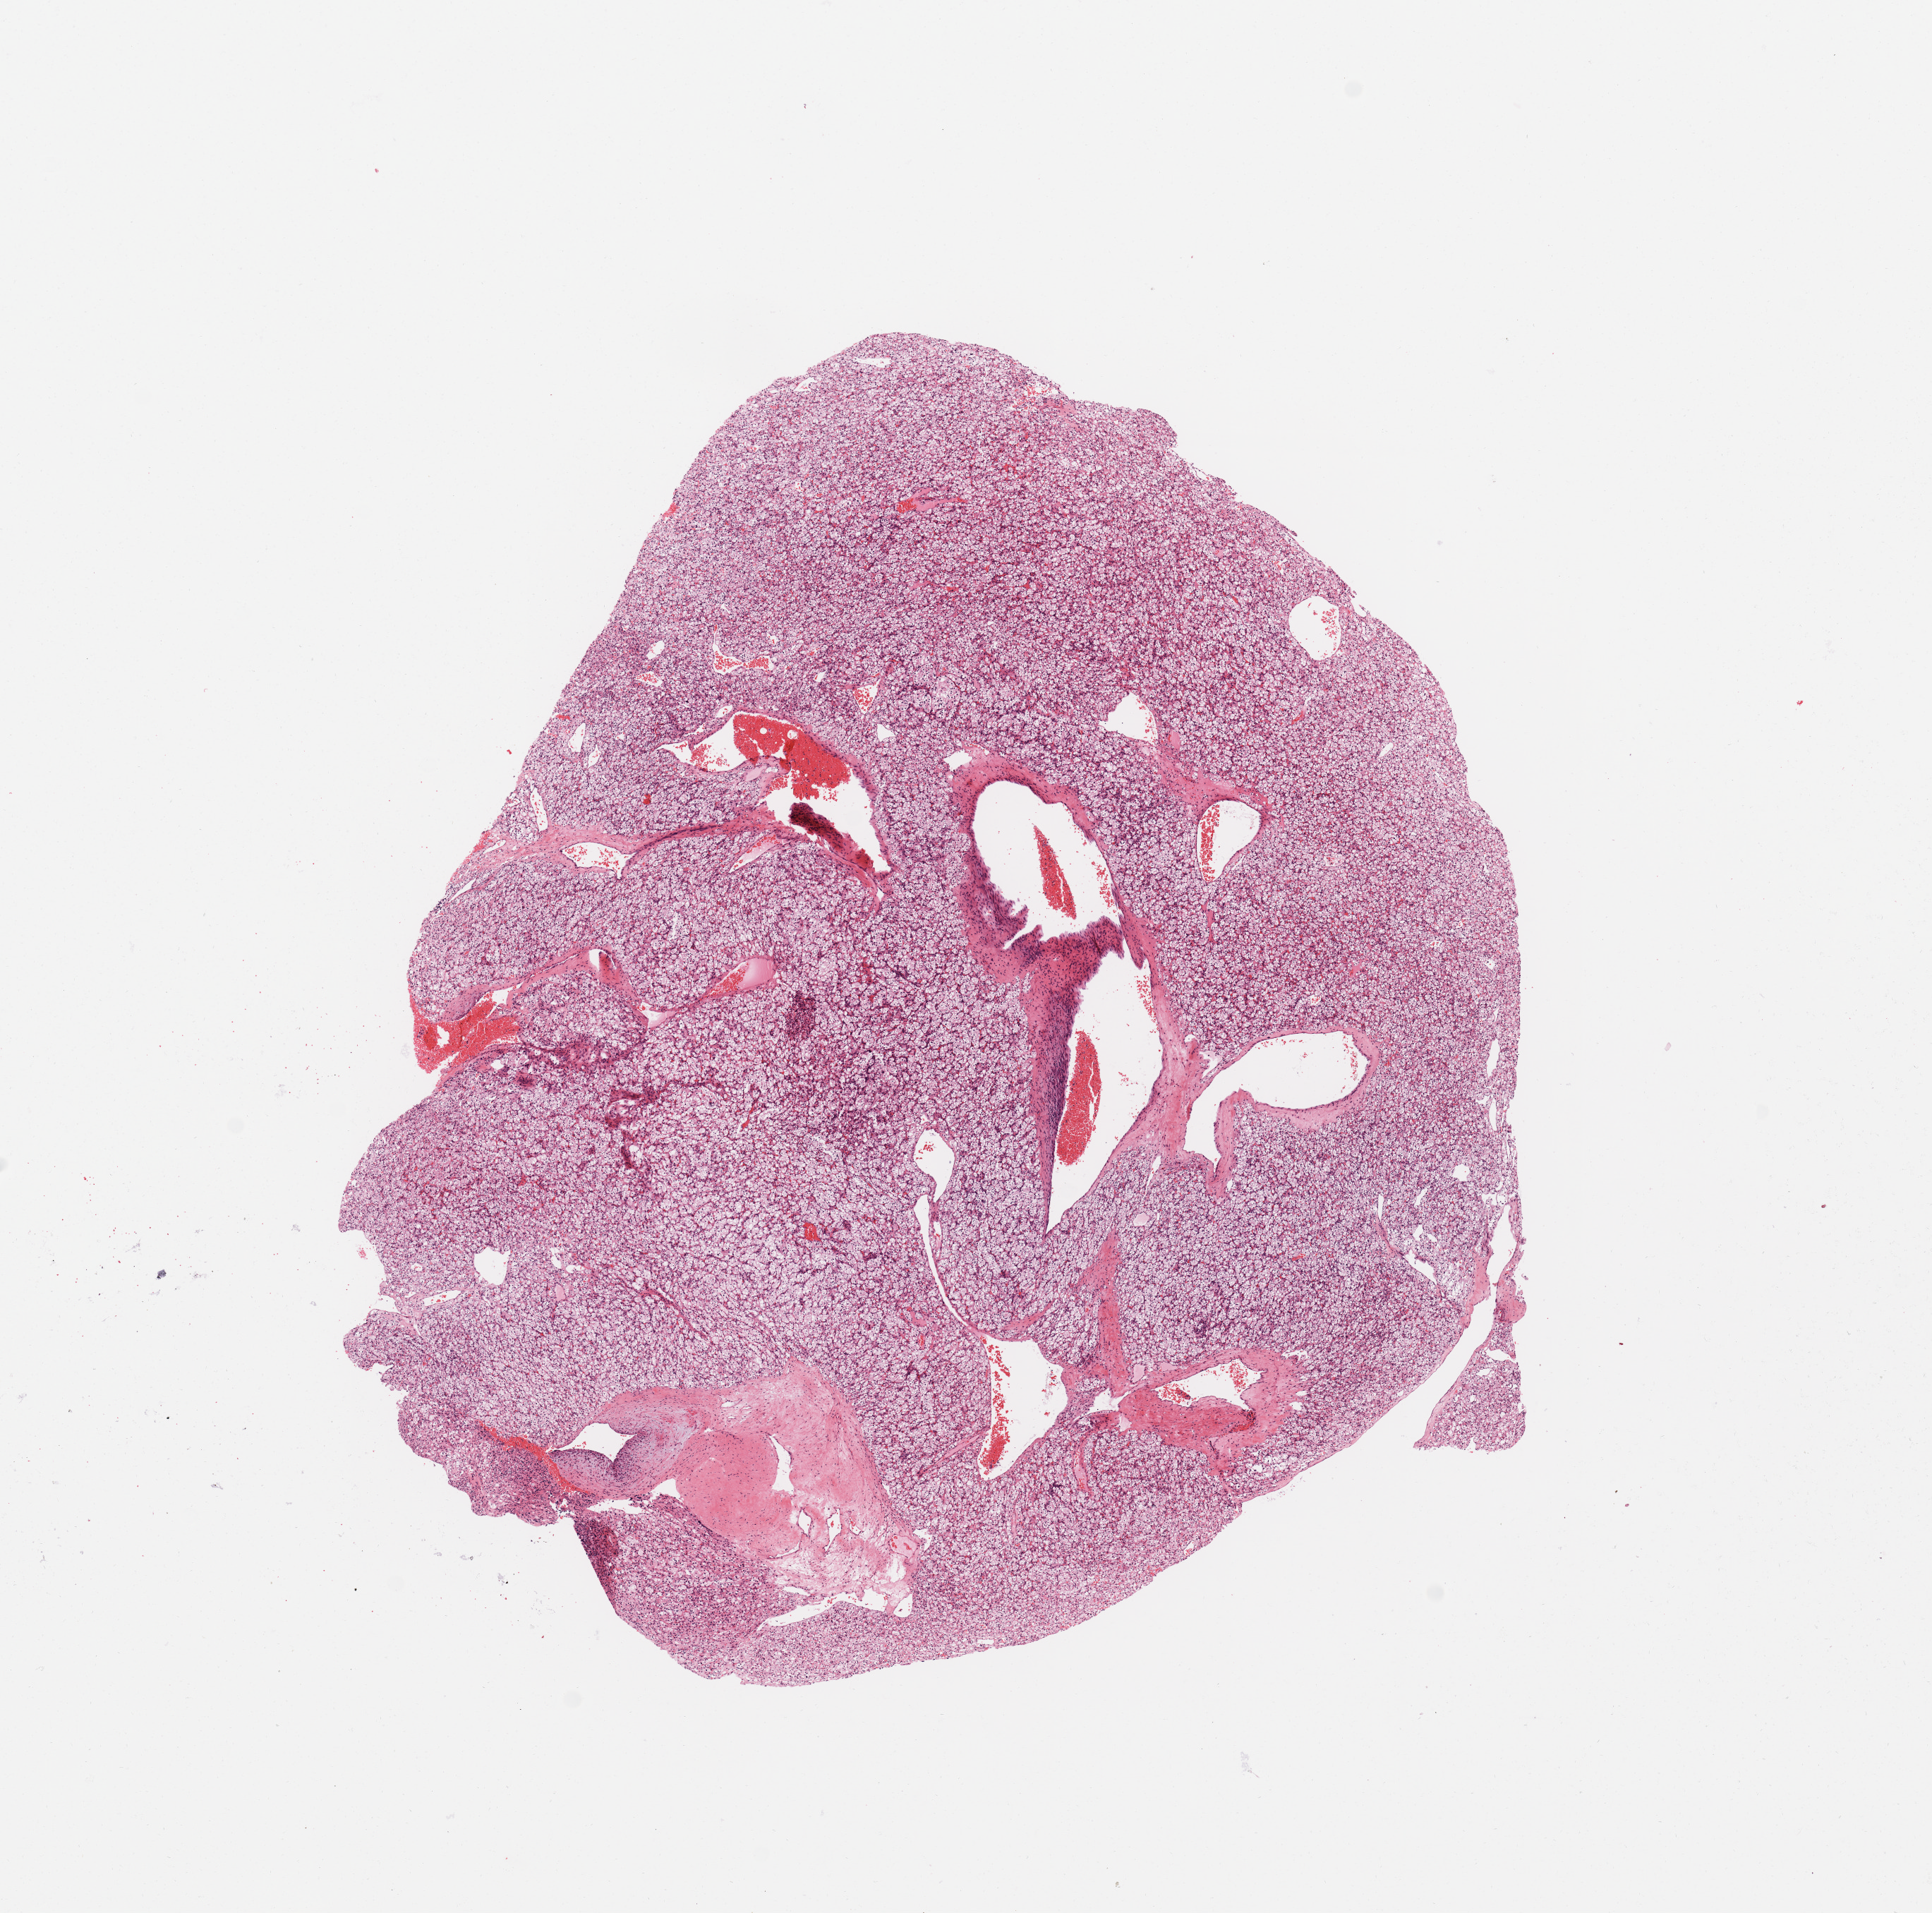
H&E-stained whole-slide image — a low-resolution overview of the entire scanned area, about 10.8 x 10.7 mm (from a 20x scan); tumour tissue sample, sampled site: kidney. 54-year-old male patient. Histologic grade: G2 (moderately differentiated). Slide review estimates, as recorded: tumour nuclei 90%, necrosis 0%.
AJCC pathologic stage: I. Histologic diagnosis: Renal cell carcinoma, NOS.